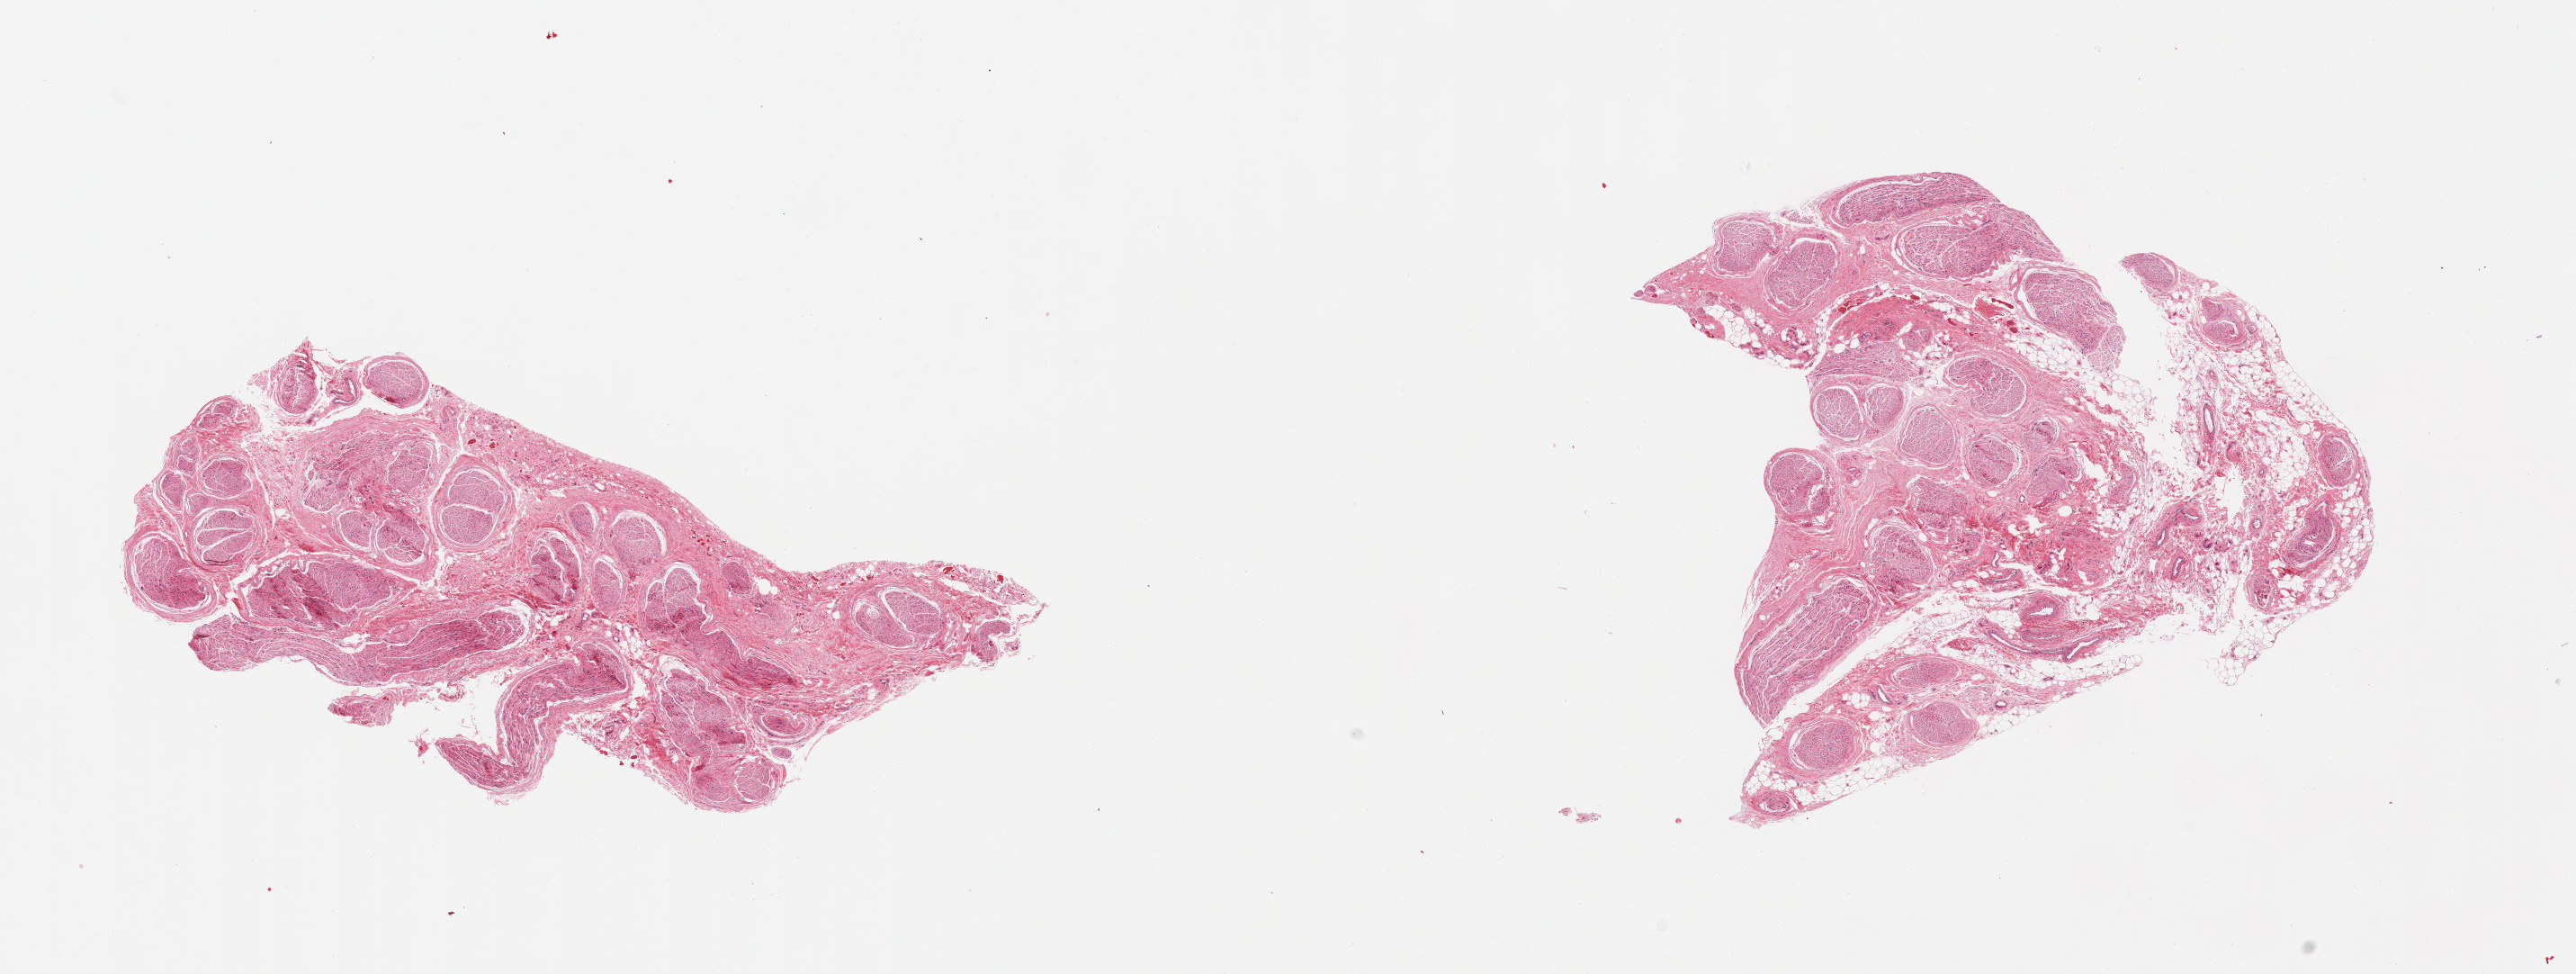
Haematoxylin and eosin whole-slide image, brightfield, whole scanned area (about 22.6 x 8.6 mm, from a 20x scan) shown as a low-resolution overview, PAXgene-fixed paraffin-embedded (PFPE) section, target tissue: tibial nerve, donor tissue sample. Donor: female.
Reviewer comment on this tissue sample: 2 pieces; 40 & 30% internal fat and/or fibrous content.